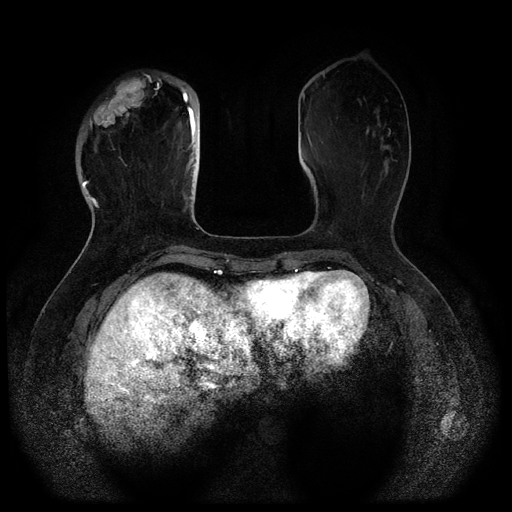
Breast MRI (dynamic contrast-enhanced, multi-phase), one axial slice; slice 30 of 116 in the series (ordered by position); dynamic contrast-enhanced series, time point 2 of 5 at this slice position (early post-contrast); 1.5 T; TE 2.6 ms, TR 5.3 ms; 2 mm slice thickness; 512 × 512 image matrix, field of view 350 × 350 mm. Female patient, age 51 years.
Outlined on this slice (semi-automatic segmentation, software-assisted and operator-edited):
- breast lesion (labelled 'tumour' in the annotation; benign lesions carry a separate 'benign' label): bounding box (x1, y1, x2, y2) in pixels: (90, 77, 146, 136)